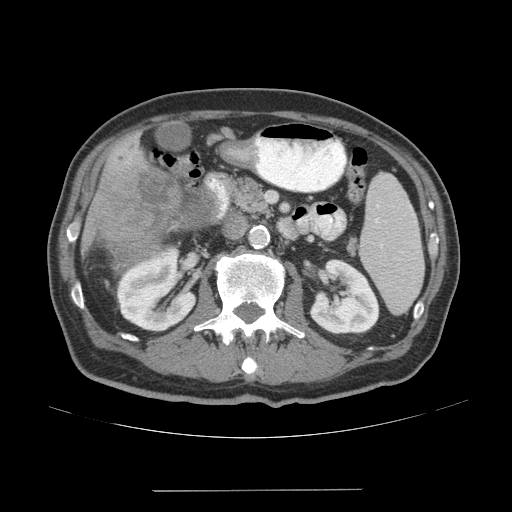
Contrast-enhanced abdominal CT (liver protocol), one axial slice. Position 12 of 77 along the scan axis. Reconstruction kernel STANDARD. 140 kVp. Soft-tissue window (W 400 / L 40 HU). 512 × 512 image matrix, field of view 400 × 400 mm. Case-level facts recorded for this patient, not image findings: diagnosis: hepatocellular carcinoma (patient treated with transarterial chemoembolisation; whether this scan precedes or follows treatment is not stated here); TNM stage (as recorded): Stage-IVA; Child-Pugh class: A; tumour differentiation: well differentiated.
Outlined on this slice (semi-automatically segmented with operator editing):
- liver parenchyma outside the tumour (the mass and vessels are separate outlines, so this box may not span the whole liver): bounding box <82,136,154,274> (left, top, right, bottom; pixels)
- mass: <104,166,217,263>